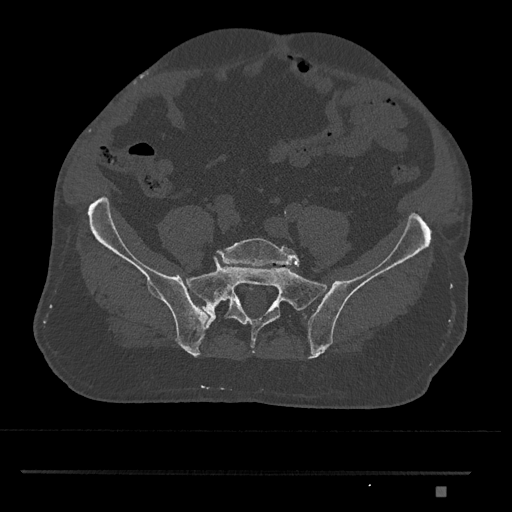
CT including the spine, one axial slice; slice 514 of 1134 in the series (ordered by position); bone window (W 1800 / L 400 HU); 0.5 mm slice thickness; 512 × 512 image matrix, field of view 429 × 429 mm. Male patient, age 65 years. Case-level facts recorded for this patient, not image findings: primary cancer: prostate.
Annotated regions visible in this slice (semi-automatic segmentation, software-assisted and operator-edited):
- L5 vertebra: bounding box (x1, y1, x2, y2) in pixels: (216, 238, 300, 267)